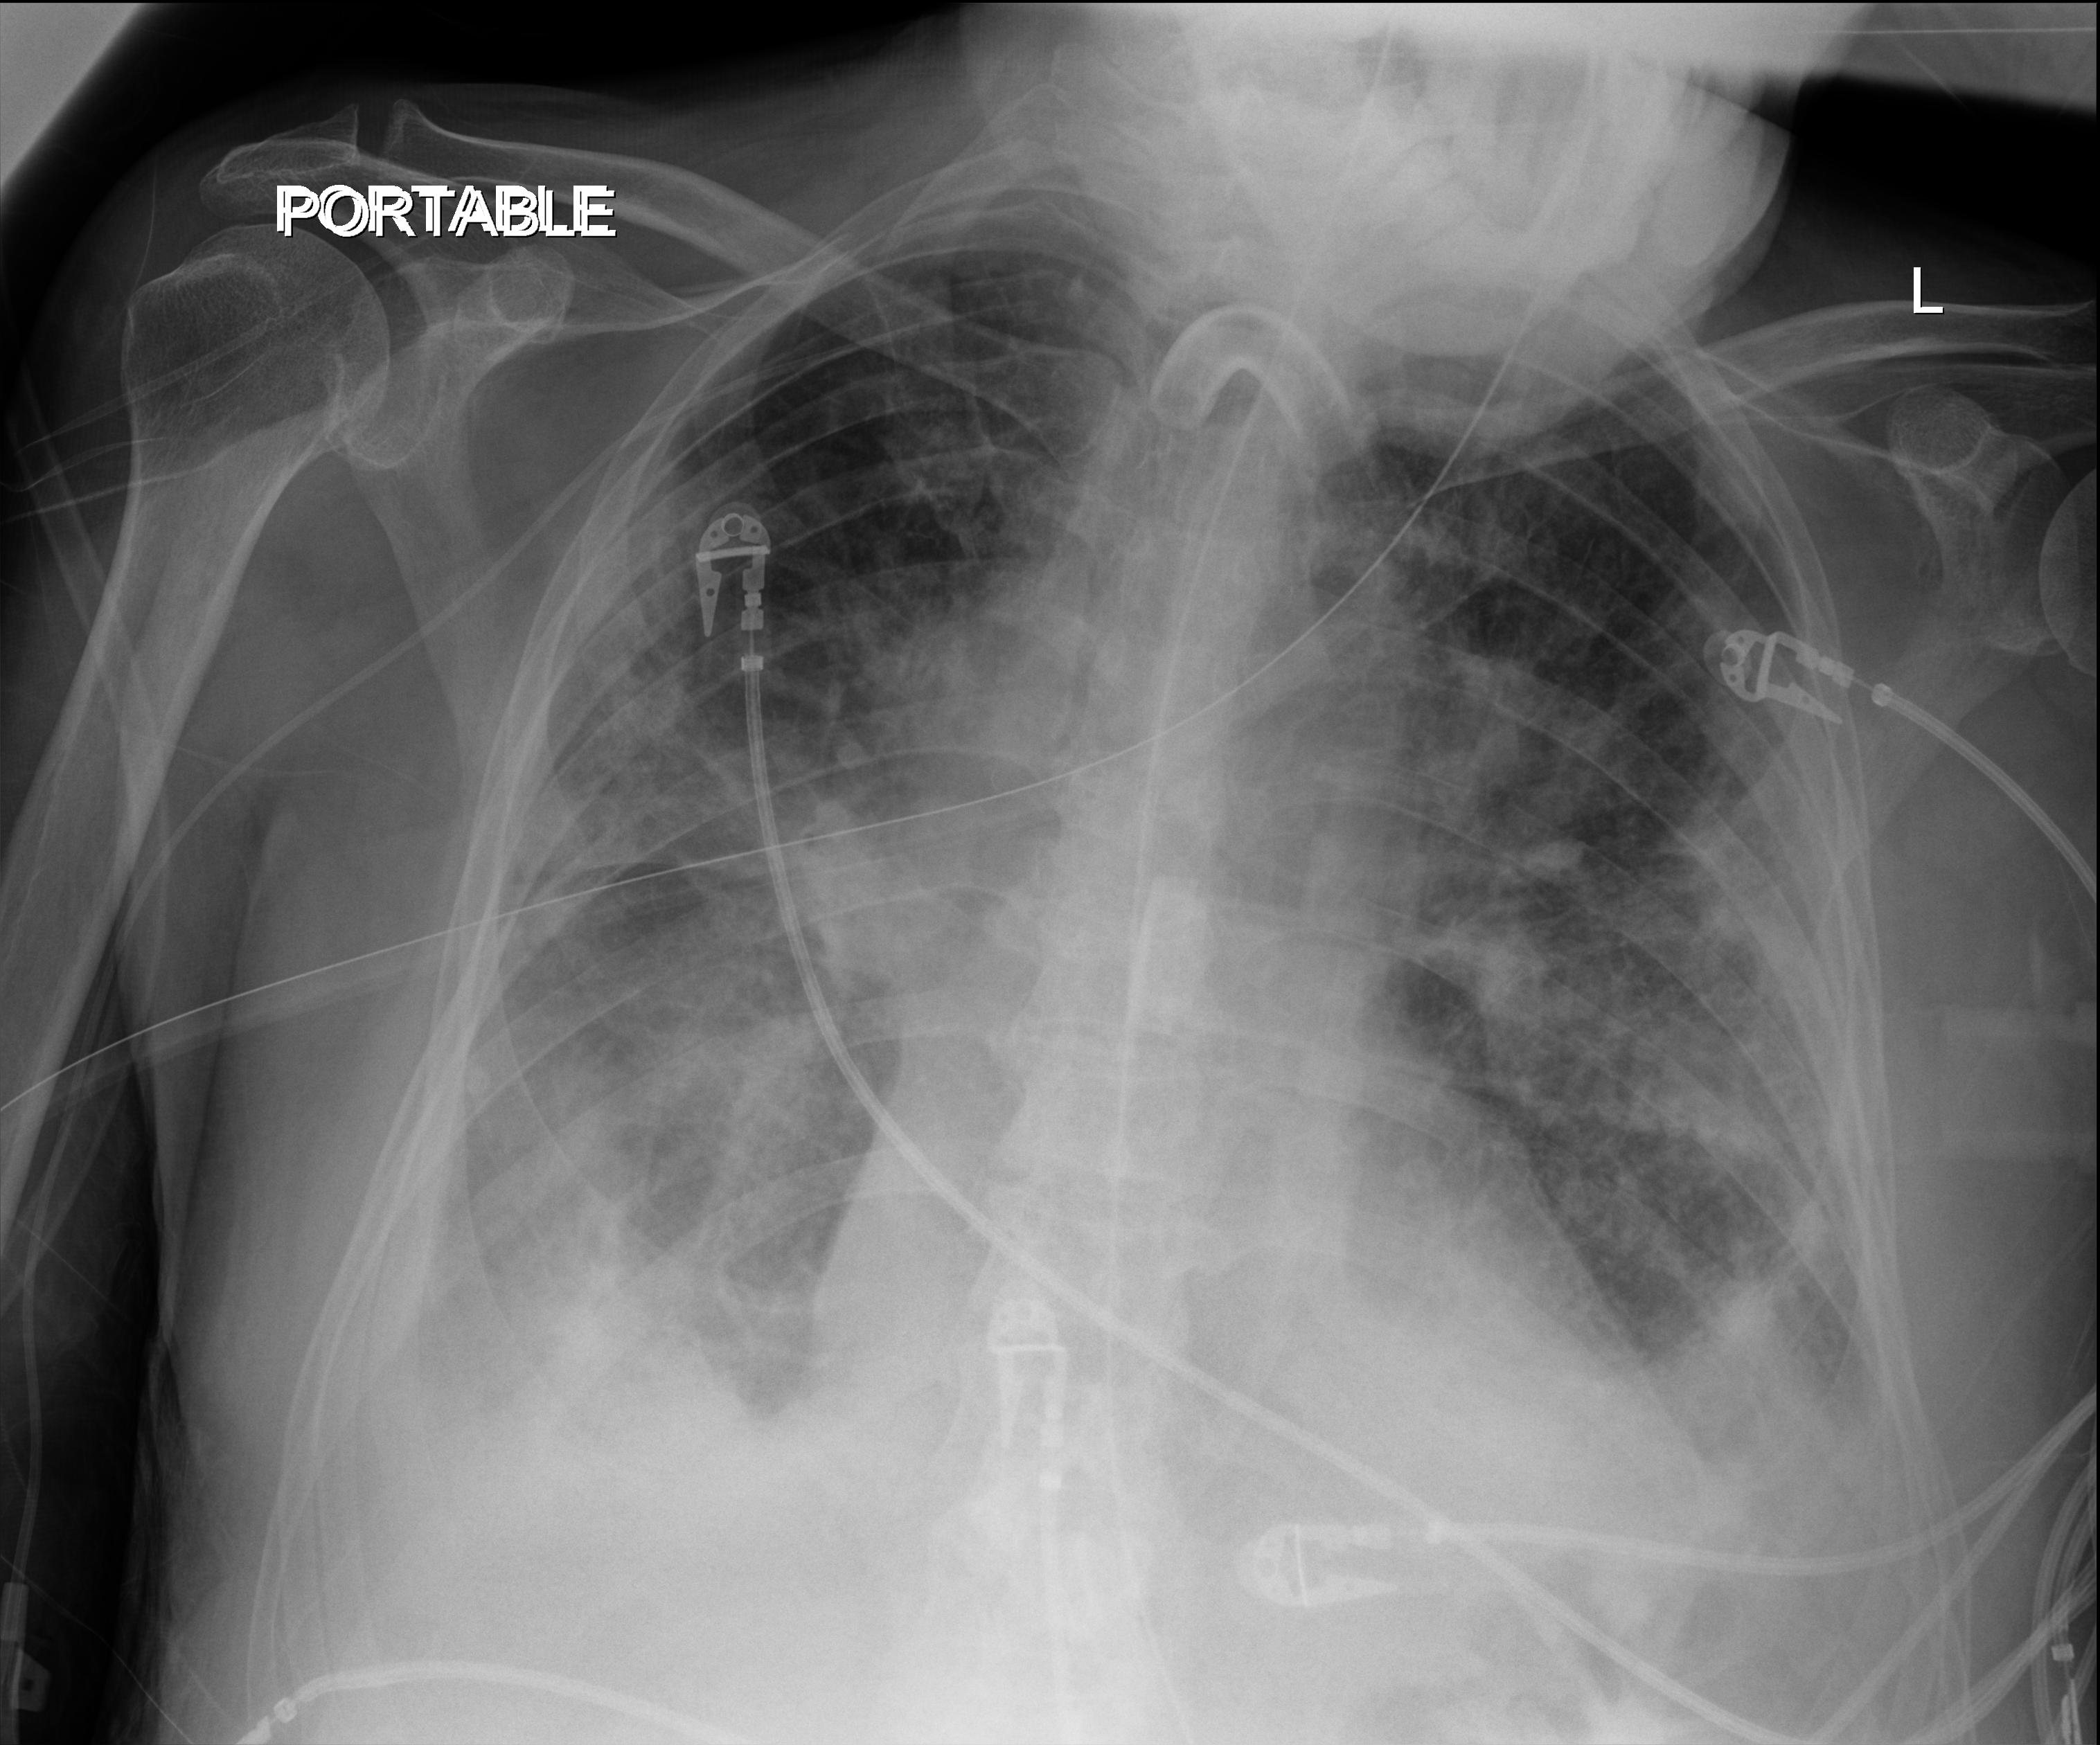
Portable chest radiograph; anteroposterior (AP) projection. Male patient hospitalised with COVID-19, age 75–90 years.
Hospital-stay facts (about this admission, not read from this image; timing relative to this image not recorded): mechanically ventilated during this hospital stay: yes.